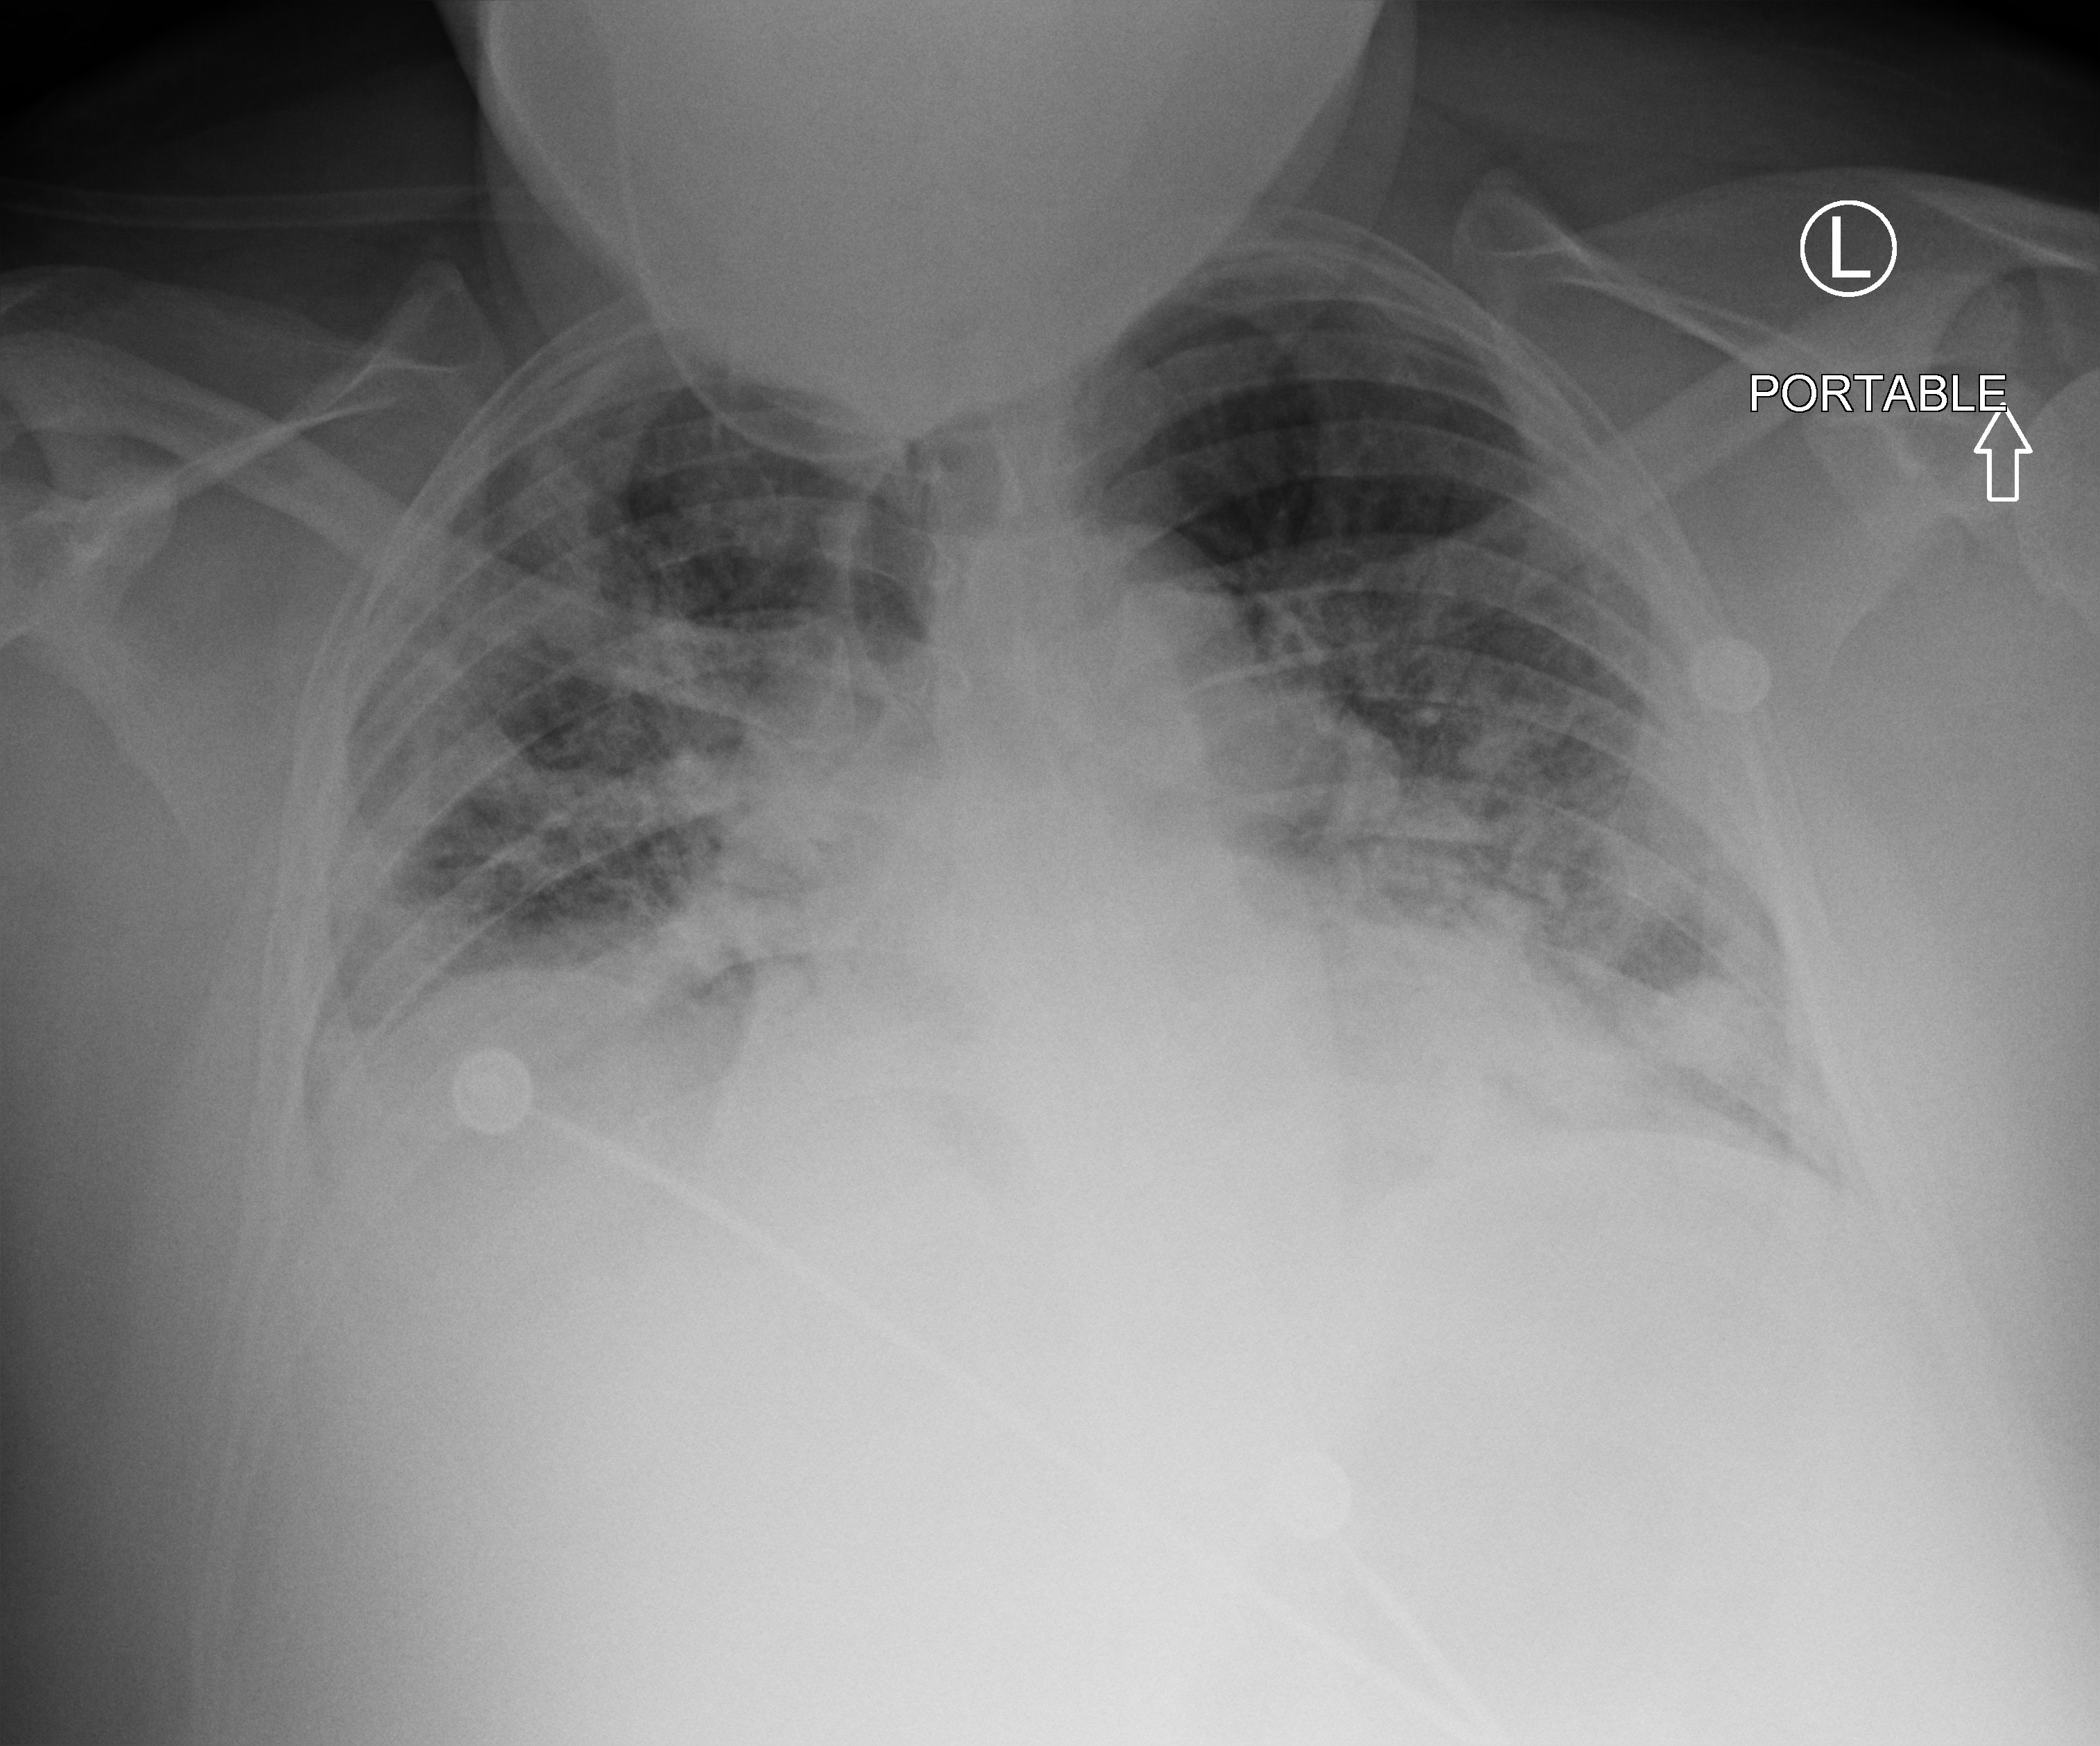
Portable chest radiograph. Patient hospitalised with COVID-19, aged 18–59 years.
Hospital-stay facts (about this admission, not read from this image; timing relative to this image not recorded): chronic kidney disease (admission record): no.